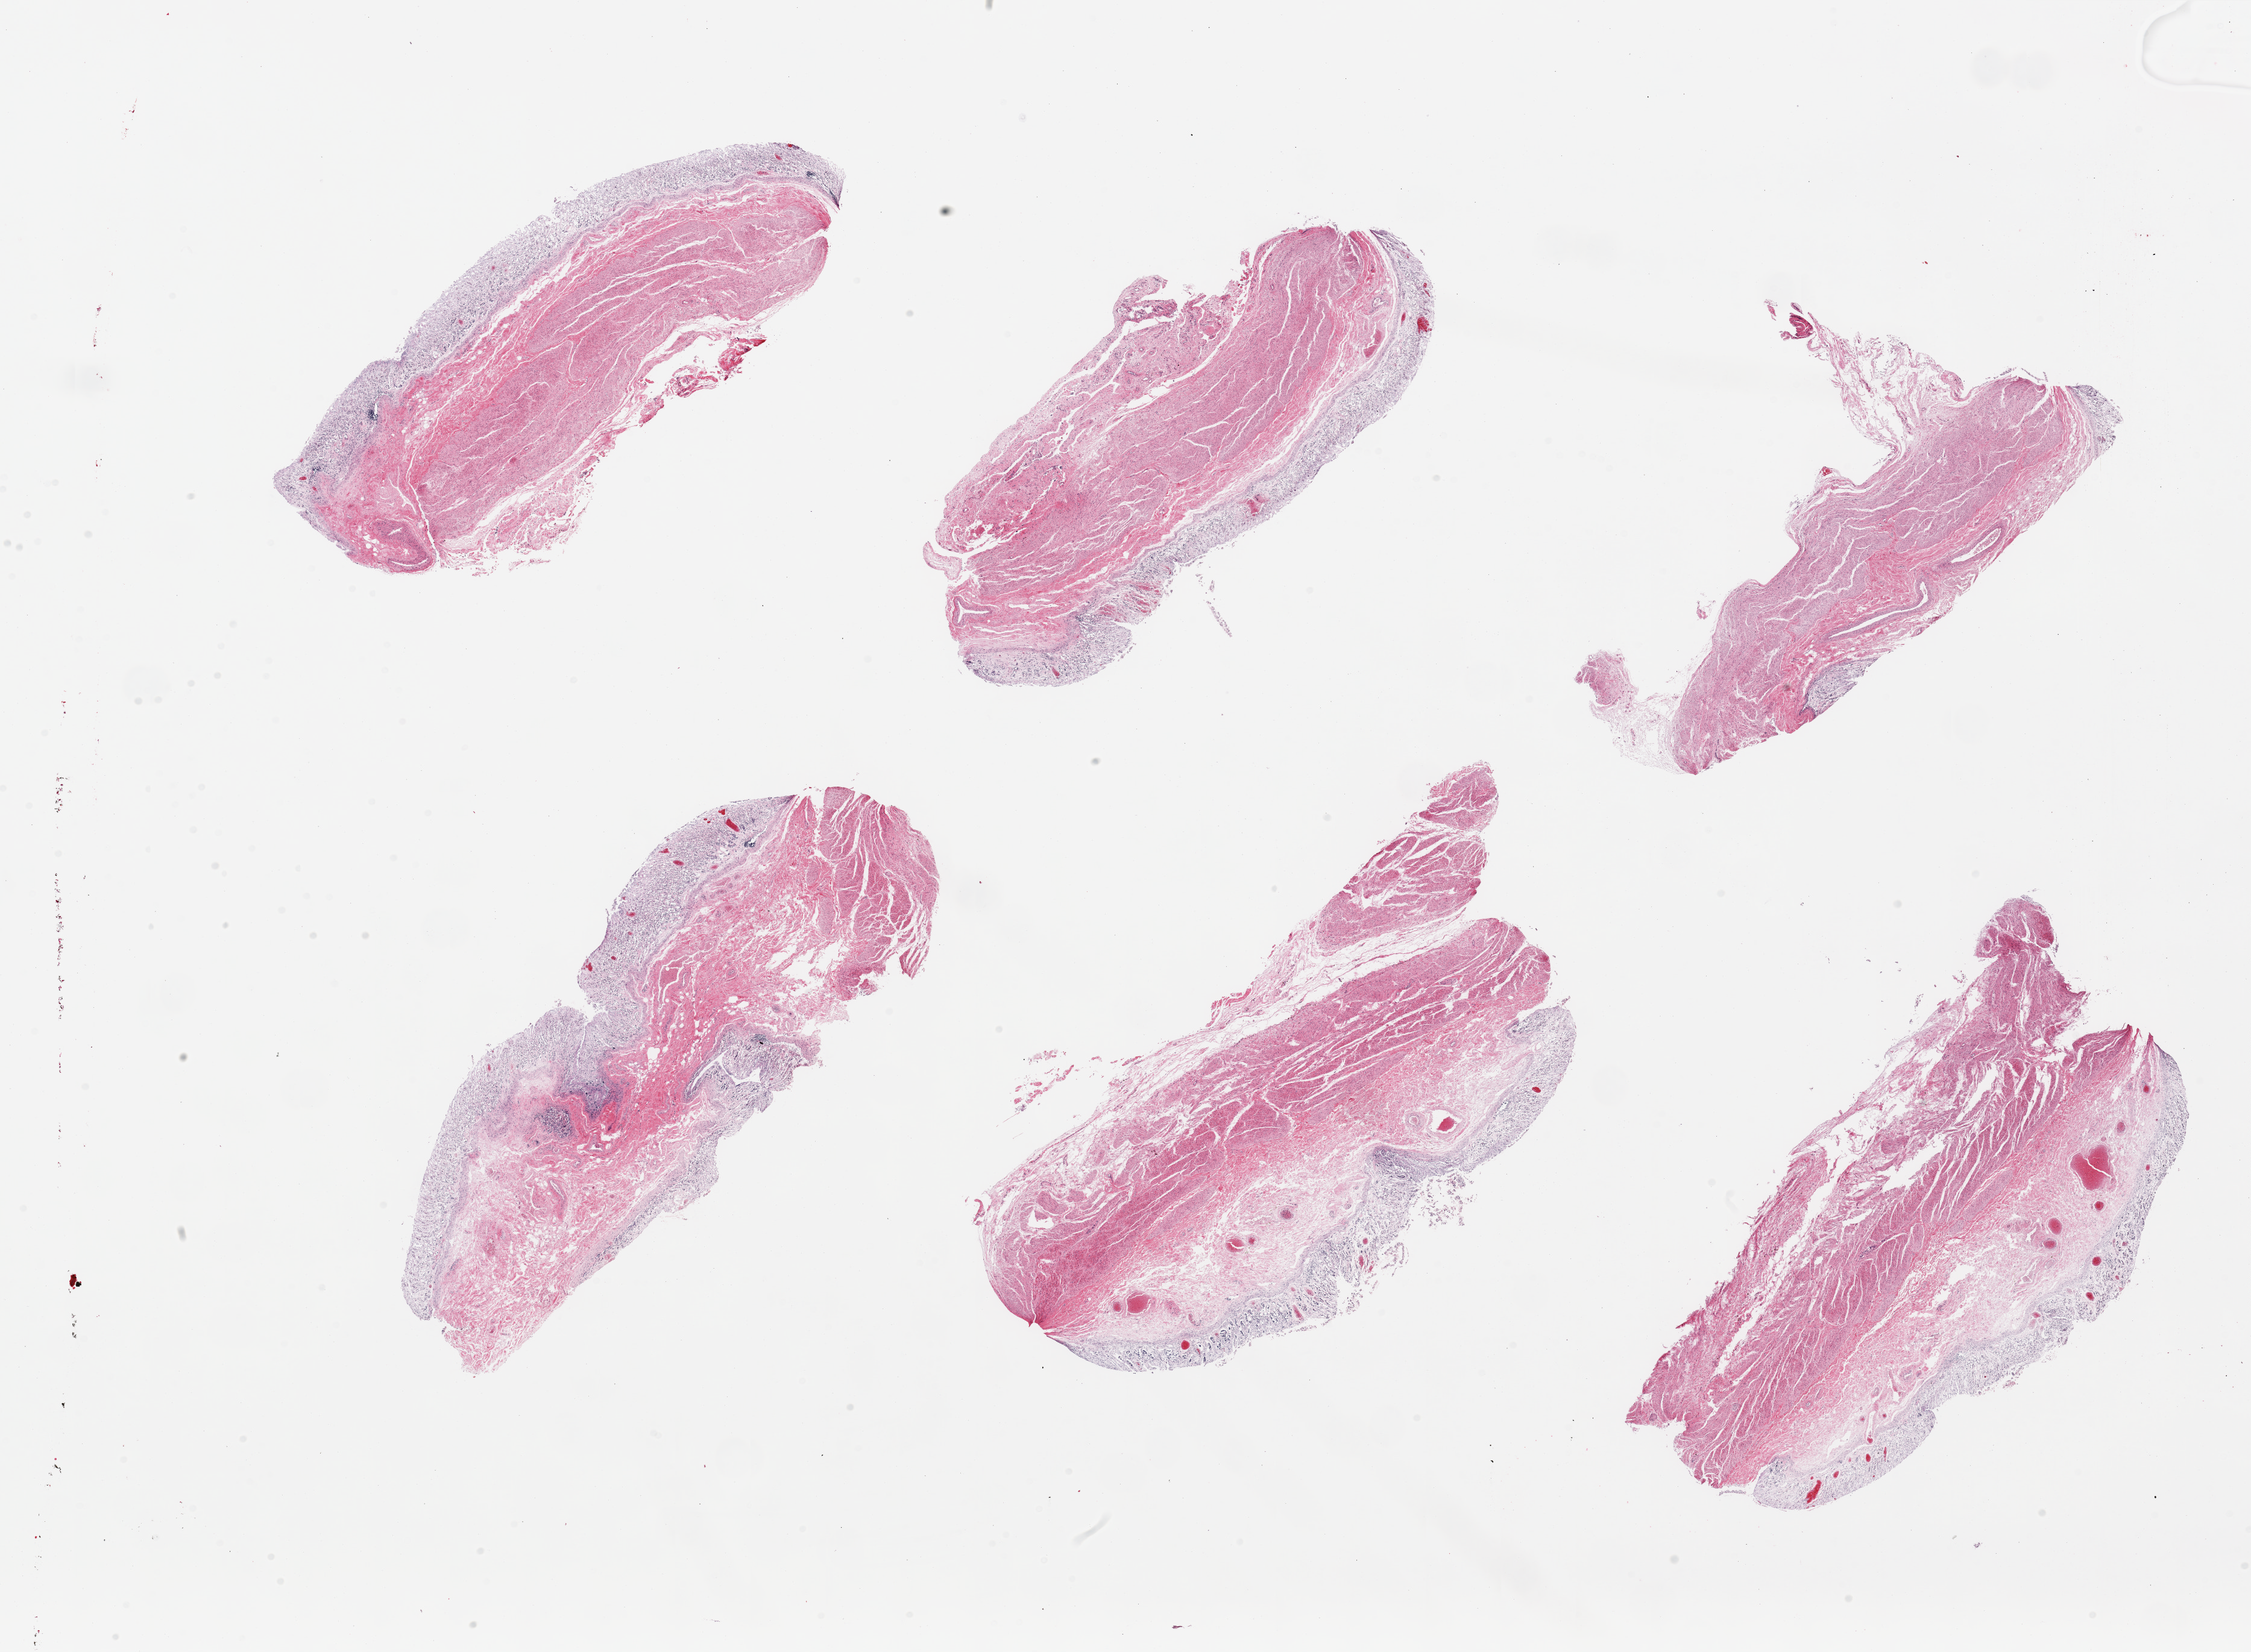
Digitized haematoxylin and eosin-stained section — shown as a low-resolution overview of the whole scanned area (about 29.5 x 21.7 mm). PAXgene-fixed, paraffin-embedded tissue. Target tissue: stomach. Donor tissue sample. Donor: female.
Reviewer comment on this tissue sample: 6 pieces, complete autolysis.